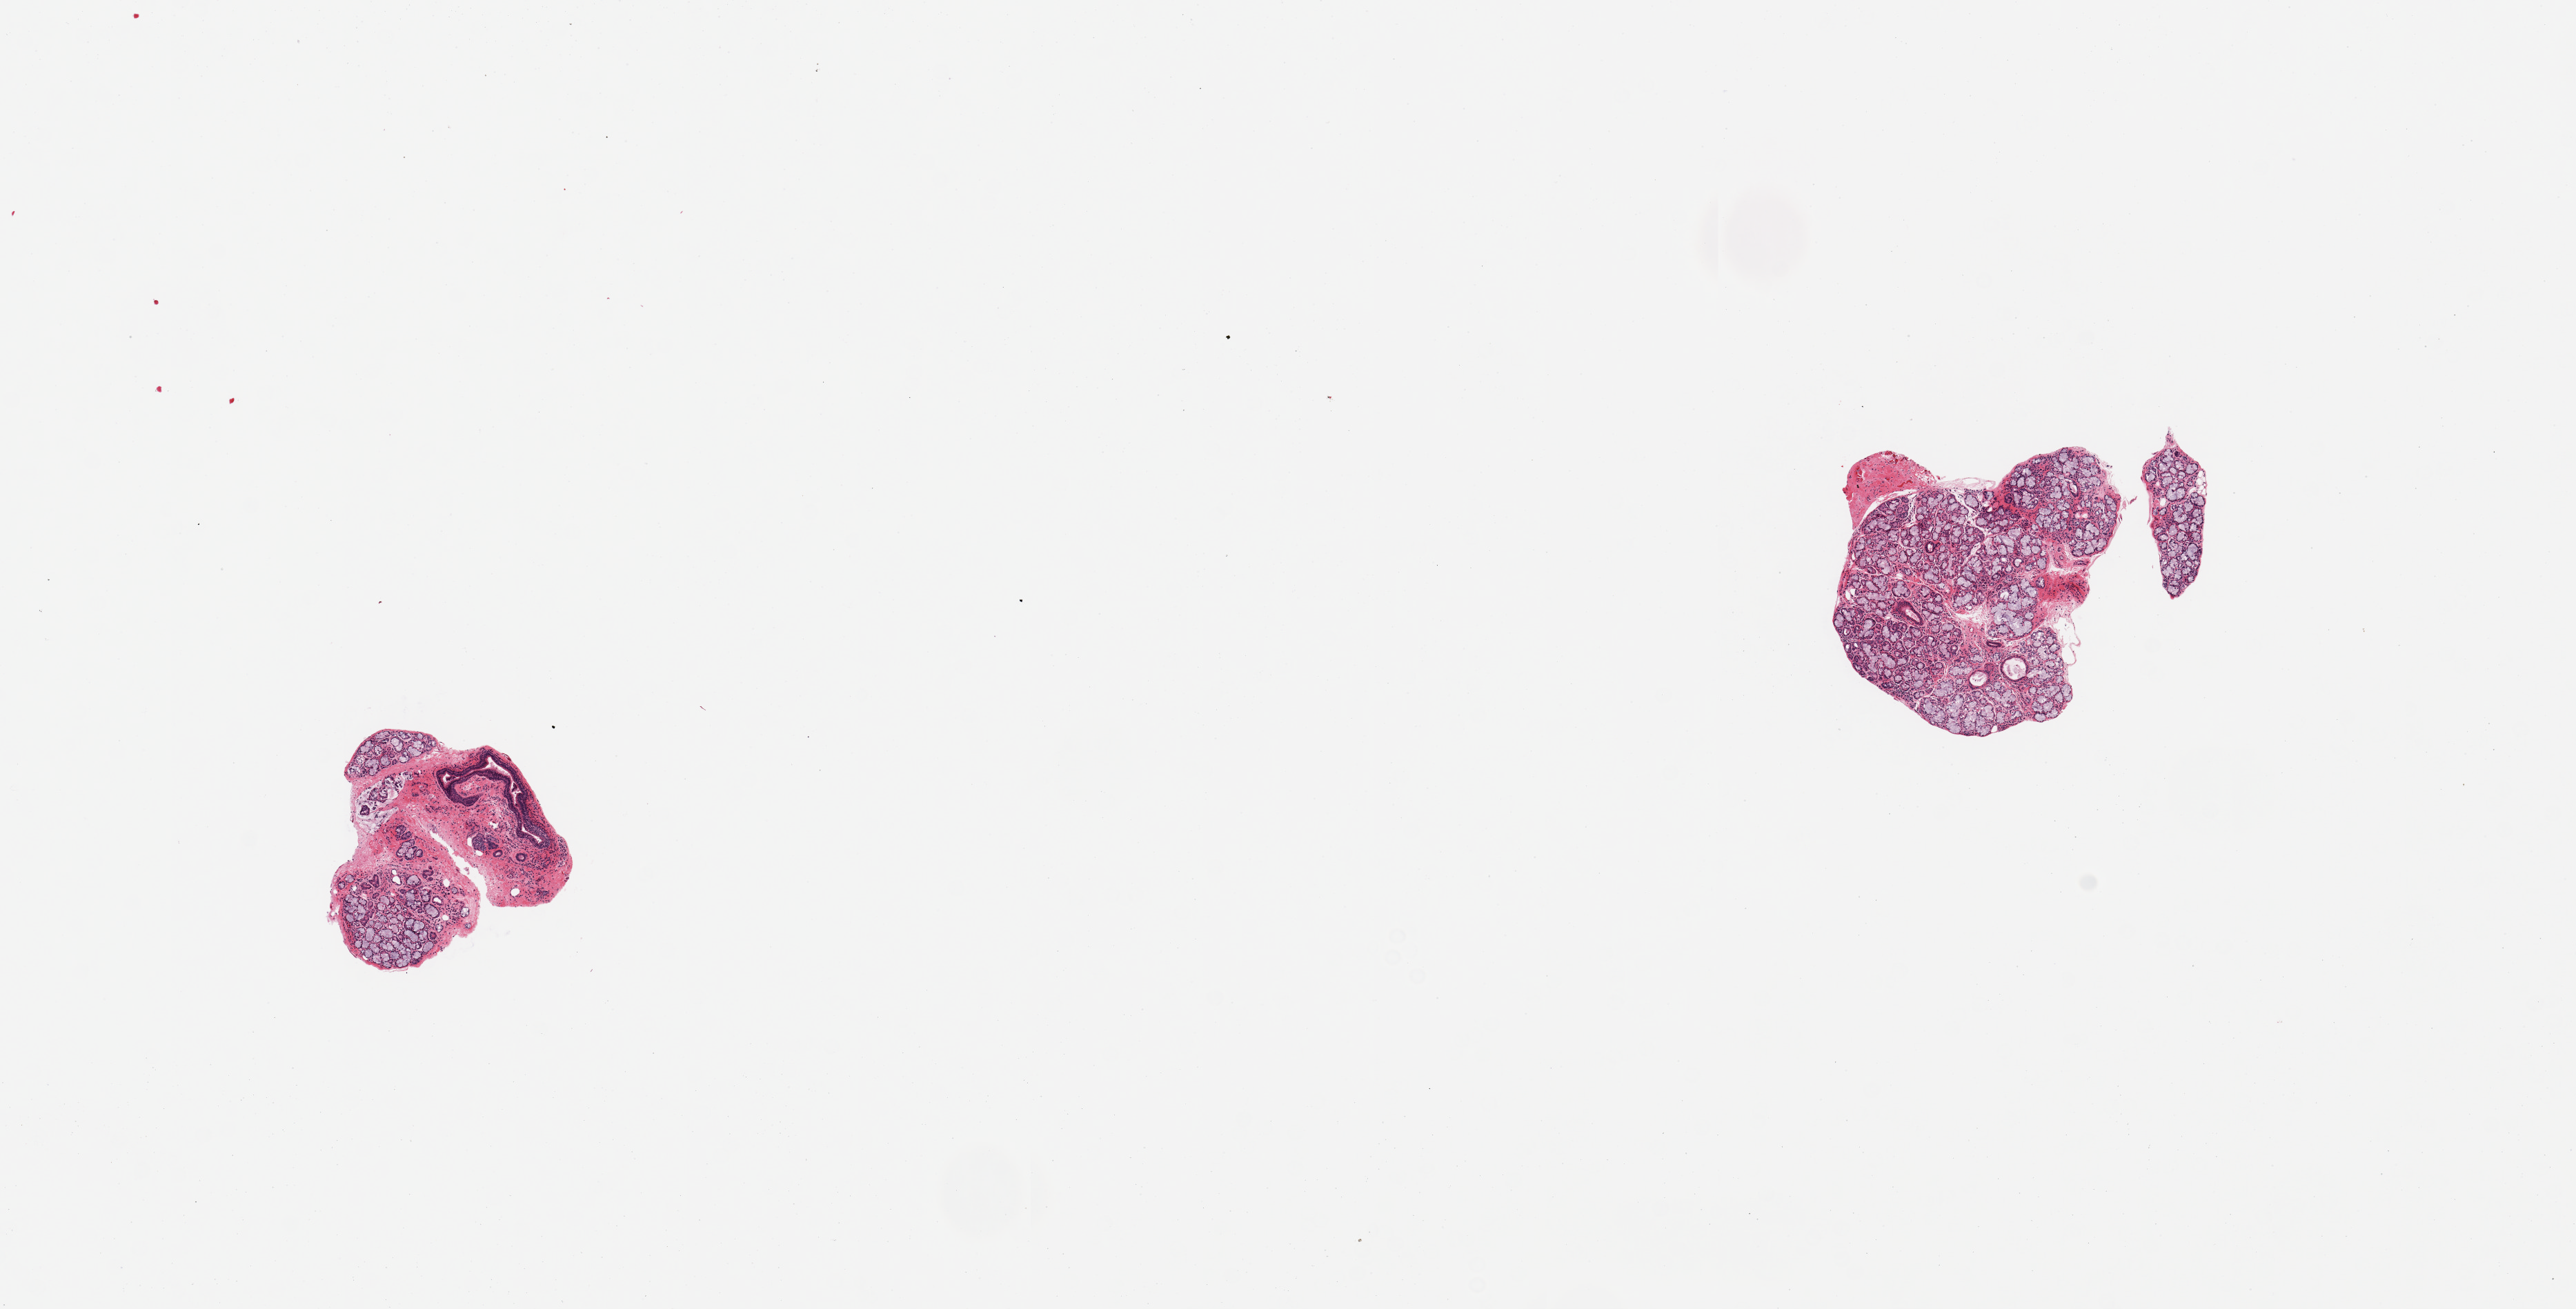
Haematoxylin and eosin whole-slide image, brightfield, a low-resolution overview of the entire scanned area, about 14.8 x 7.5 mm, PAXgene-fixed, paraffin-embedded tissue, target tissue: minor salivary gland, tissue donor sample. Donor sex: male.
• pathologist's review note for this sample: 2 pieces; well trimmed